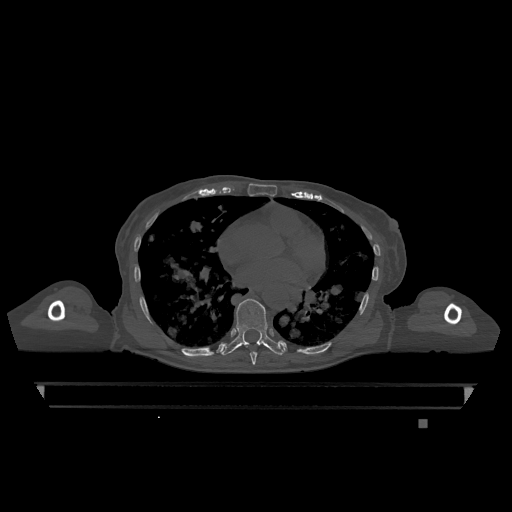
CT including the spine, one axial slice. Position 704 of 1317 along the scan axis. Bone window (W 1800 / L 400 HU). 0.5 mm slice thickness. 512 × 512 image matrix, field of view 500 × 500 mm. Female patient, age 74 years. From the clinical record (not read from this slice): primary cancer: lung; vertebrae with lytic lesions (as recorded): T1, T4, T5, T6, L4, L5.
Annotated regions visible in this slice (semi-automatically segmented with operator editing):
- T7 vertebra: bounding box [x1, y1, x2, y2] px = [250, 352, 257, 365]
- T9 vertebra: [221, 298, 284, 355]